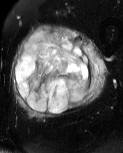
MRI of an extremity soft-tissue mass, one axial slice. Slice 23 of 60 in the series (ordered by position). T2-weighted fat-saturated. MR volume resampled by the dataset authors to the PET/CT grid (not the native acquisition matrix). 3.27 mm slice thickness. 123 × 153 image matrix. Male patient. From the clinical record (not read from this slice): histological type: pleiomorphic liposarcoma; grade: high; site of the primary tumour: left thigh.
Outlined on this slice (expert contour drawn on MRI and transferred to this co-registered scan by the dataset authors):
- gross tumour volume including surrounding oedema: bounding box (x1, y1, x2, y2) in pixels: (11, 26, 110, 119)
- gross tumour volume (mass): (15, 31, 92, 114)